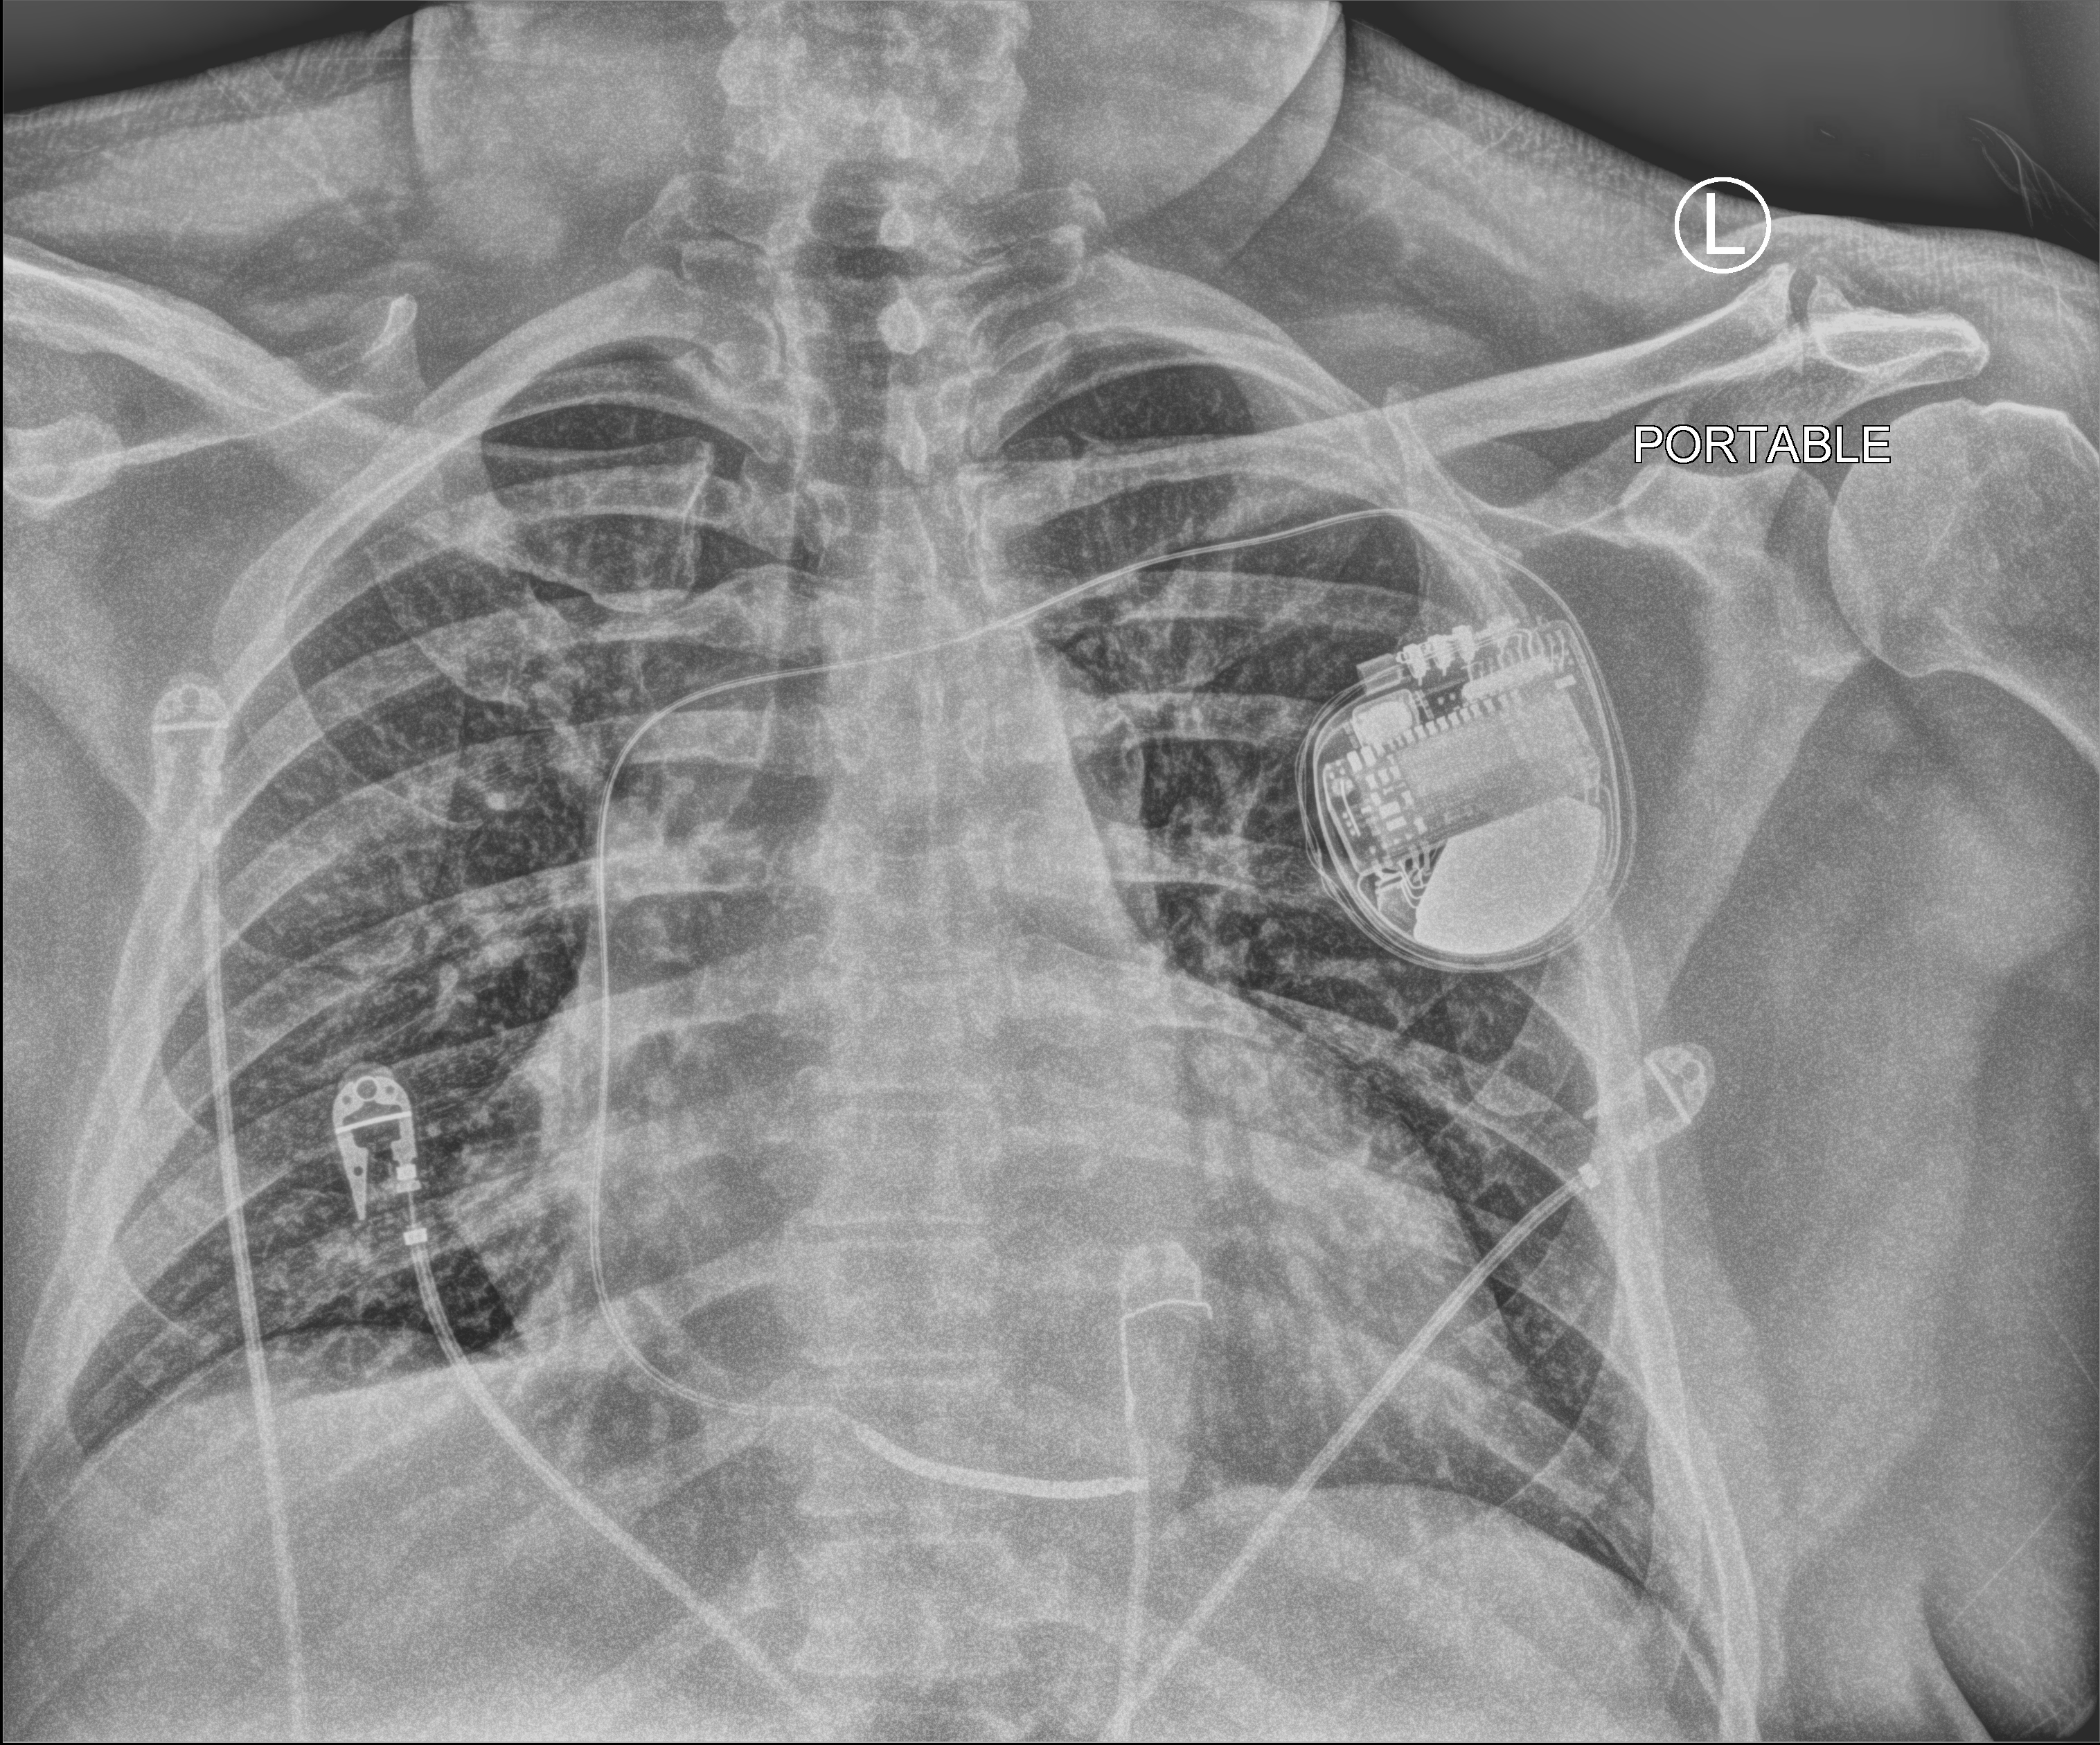
Portable chest radiograph, anteroposterior (AP) projection. Patient hospitalised with COVID-19; male, aged 18–59 years.
Admission-level facts for this patient (not findings on this image; timing relative to this image not recorded):
- mechanically ventilated during this hospital stay: no